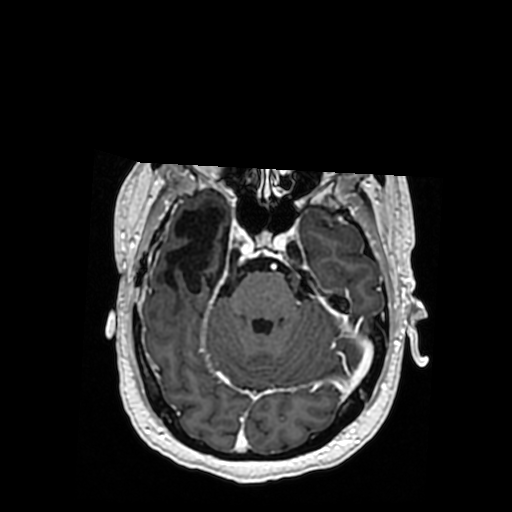
Brain MRI from a brain-tumour surgery series, one axial slice. Slice 240 of 364 in the series (ordered by position). T1-weighted post-contrast. 0.5 mm slice thickness. 512 × 512 image matrix, field of view 260 × 260 mm. From the clinical record (not read from this slice): histopathology: Oligodendroglioma; WHO grade: 3.
Outlined on this slice (outlined manually by an expert reader):
- previous resection cavity: bounding box <165,207,228,293> (left, top, right, bottom; pixels)